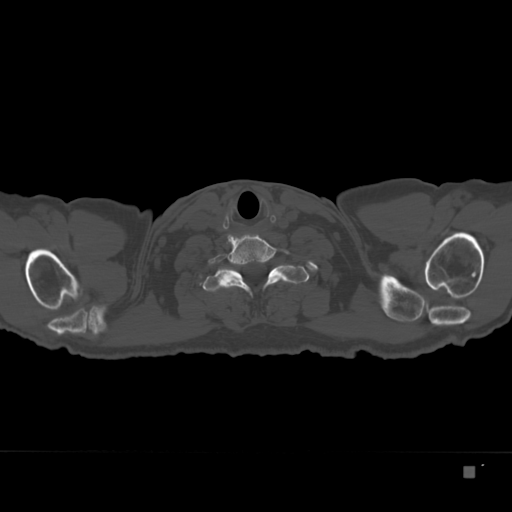
CT including the spine, one axial slice. Position 323 of 332 along the scan axis. 120 kVp. Bone window (W 1800 / L 400 HU). 512 × 512 image matrix, field of view 389 × 389 mm. Male patient, age 72 years. From the clinical record (not read from this slice): primary cancer: skeletal.
Annotated regions visible in this slice (semi-automatically segmented with operator editing):
- T1 vertebra: bounding box [x1, y1, x2, y2] px = [202, 258, 310, 293]